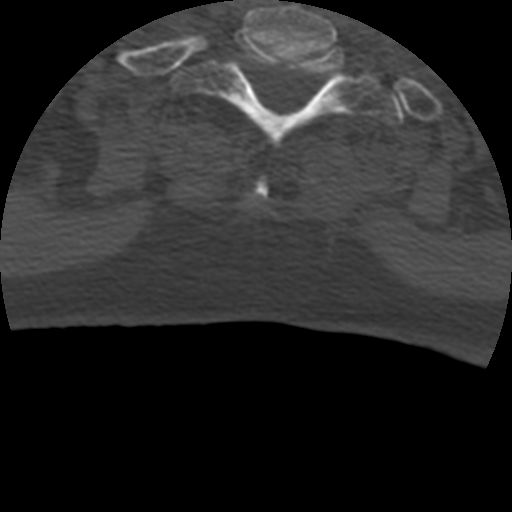
CT including the spine, one axial slice; position 386 of 399 along the scan axis; bone window (W 1800 / L 400 HU); 512 × 512 image matrix, field of view 160 × 160 mm. Patient age 69 years. Case-level facts recorded for this patient, not image findings: primary cancer: prostate.
Structures marked on this image (semi-automatic segmentation, software-assisted and operator-edited):
- T1 vertebra: bounding box (x1, y1, x2, y2) in pixels: (180, 29, 403, 149)